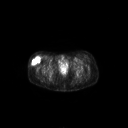
FDG PET of an extremity soft-tissue mass (from a PET/CT study), one axial slice; position 58 of 267 along the scan axis; 128 × 128 image matrix, field of view 700 × 700 mm. Patient: female, 34 years. Case-level facts recorded for this patient, not image findings: histological type: synovial sarcoma; grade: intermediate; site of the primary tumour: right thigh.
Annotated regions visible in this slice (expert contour drawn on MRI and transferred to this co-registered scan by the dataset authors):
- gross tumour volume including surrounding oedema: bounding box [x1, y1, x2, y2] px = [31, 56, 40, 65]
- gross tumour volume (mass): [31, 56, 40, 65]